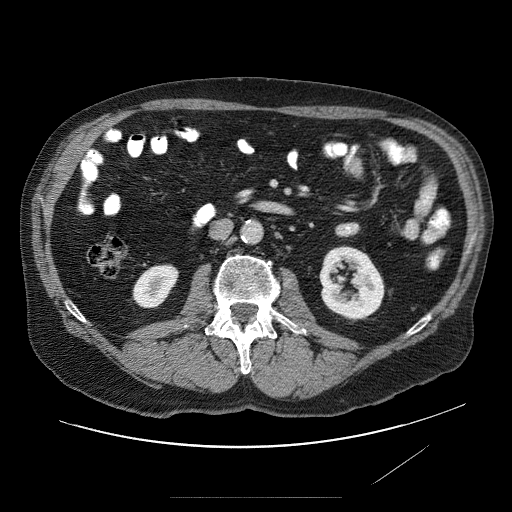
Contrast-enhanced abdominal CT (liver protocol), one axial slice. Position 3 of 89 along the scan axis. 120 kVp. Soft-tissue window (W 400 / L 40 HU). 2.5 mm slice thickness. 512 × 512 image matrix. Case-level facts recorded for this patient, not image findings: diagnosis: hepatocellular carcinoma (patient treated with transarterial chemoembolisation; whether this scan precedes or follows treatment is not stated here); TNM stage (as recorded): Stage-IVA; Child-Pugh class: A; tumour differentiation: moderately differentiated; tumour nodularity: multinodular.
Outlined on this slice (semi-automatic segmentation, software-assisted and operator-edited):
- liver parenchyma outside the tumour (the mass and vessels are separate outlines, so this box may not span the whole liver): bounding box [x1, y1, x2, y2] px = [80, 170, 100, 218]